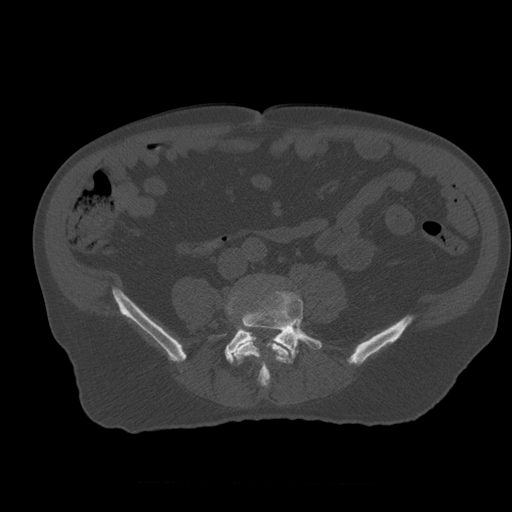
CT including the spine, one axial slice. Position 151 of 399 along the scan axis. 120 kVp. Bone window (W 1800 / L 400 HU). 1.25 mm slice thickness. 512 × 512 image matrix, field of view 407 × 407 mm. Patient age 73 years. From the clinical record (not read from this slice): primary cancer: prostate; vertebrae with lytic lesions (as recorded): L2.
Structures marked on this image (semi-automatically segmented with operator editing):
- L4 vertebra: box from (x=227, y=290) to (x=289, y=388) px
- L5 vertebra: (x=225, y=293)–(x=322, y=383)